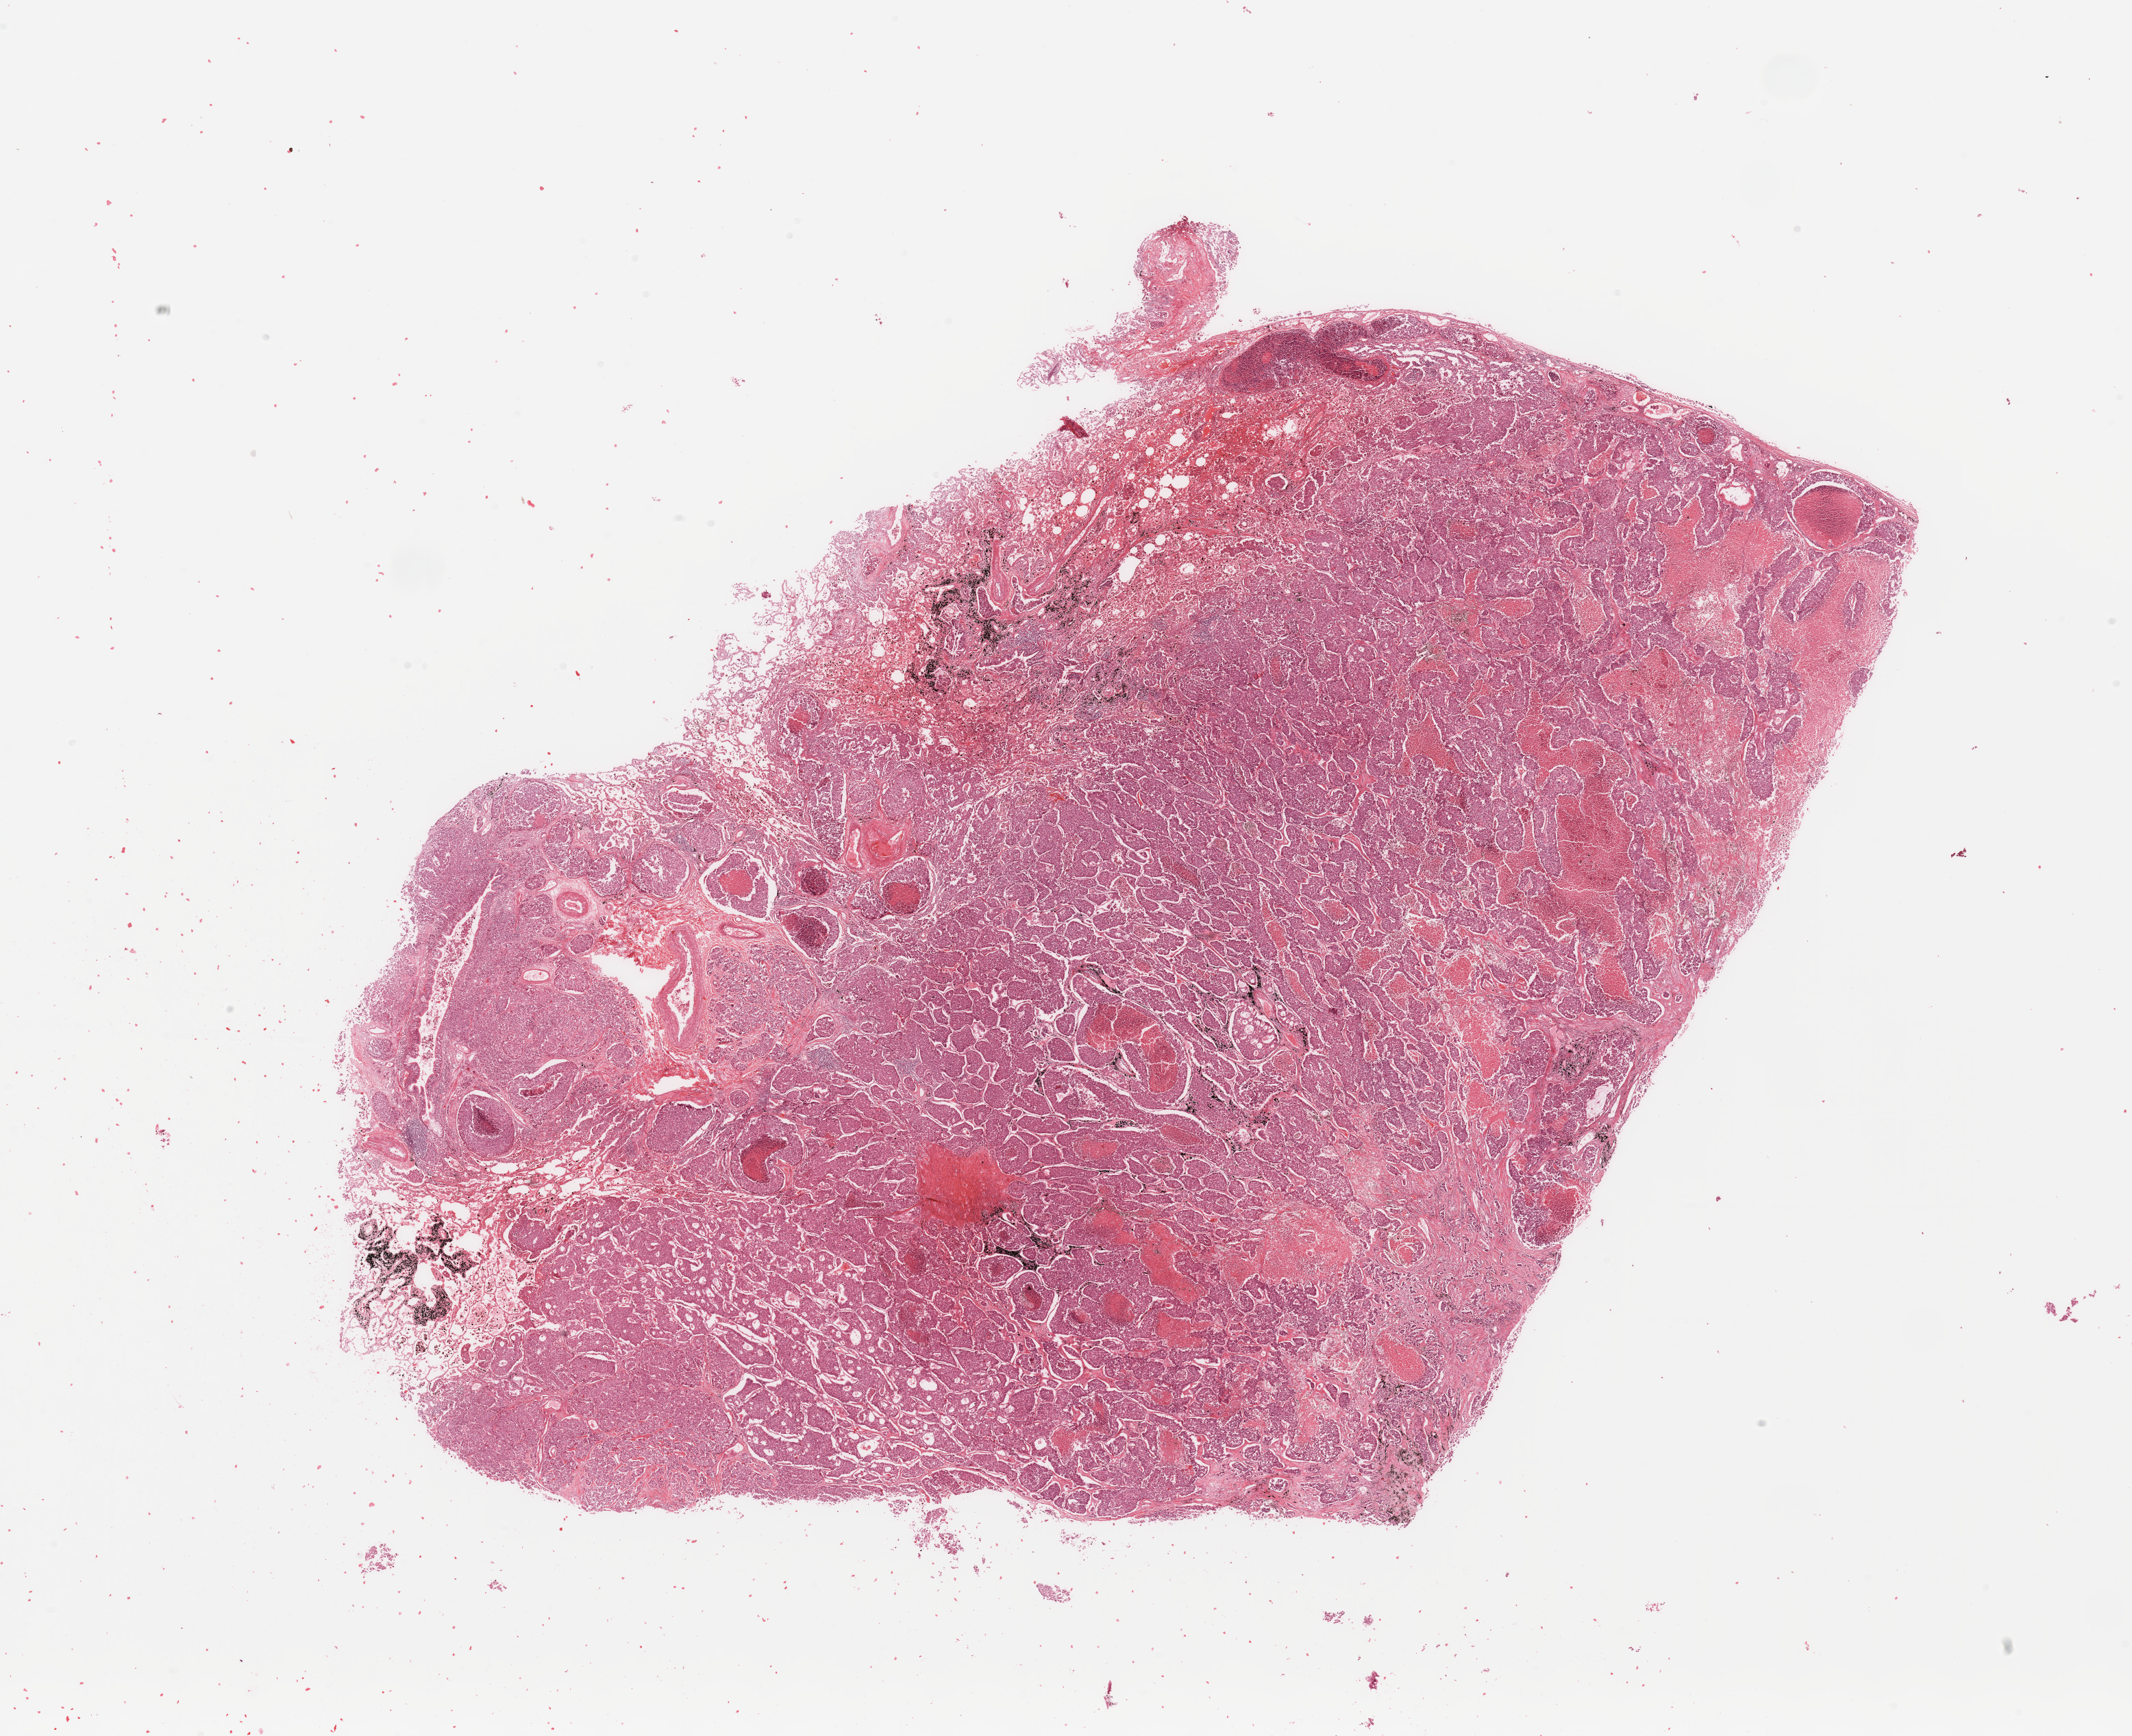
Digitized H&E tissue section (whole slide), low-resolution overview of the scanned area, about 24.6 x 20.0 mm (slide scanned at 20x). Tumour tissue sample, lung. Patient: male, age 56 years. Histologic grade: G3 (poorly differentiated).
- histologic diagnosis: Adenocarcinoma, NOS
- AJCC pathologic stage: IIIA